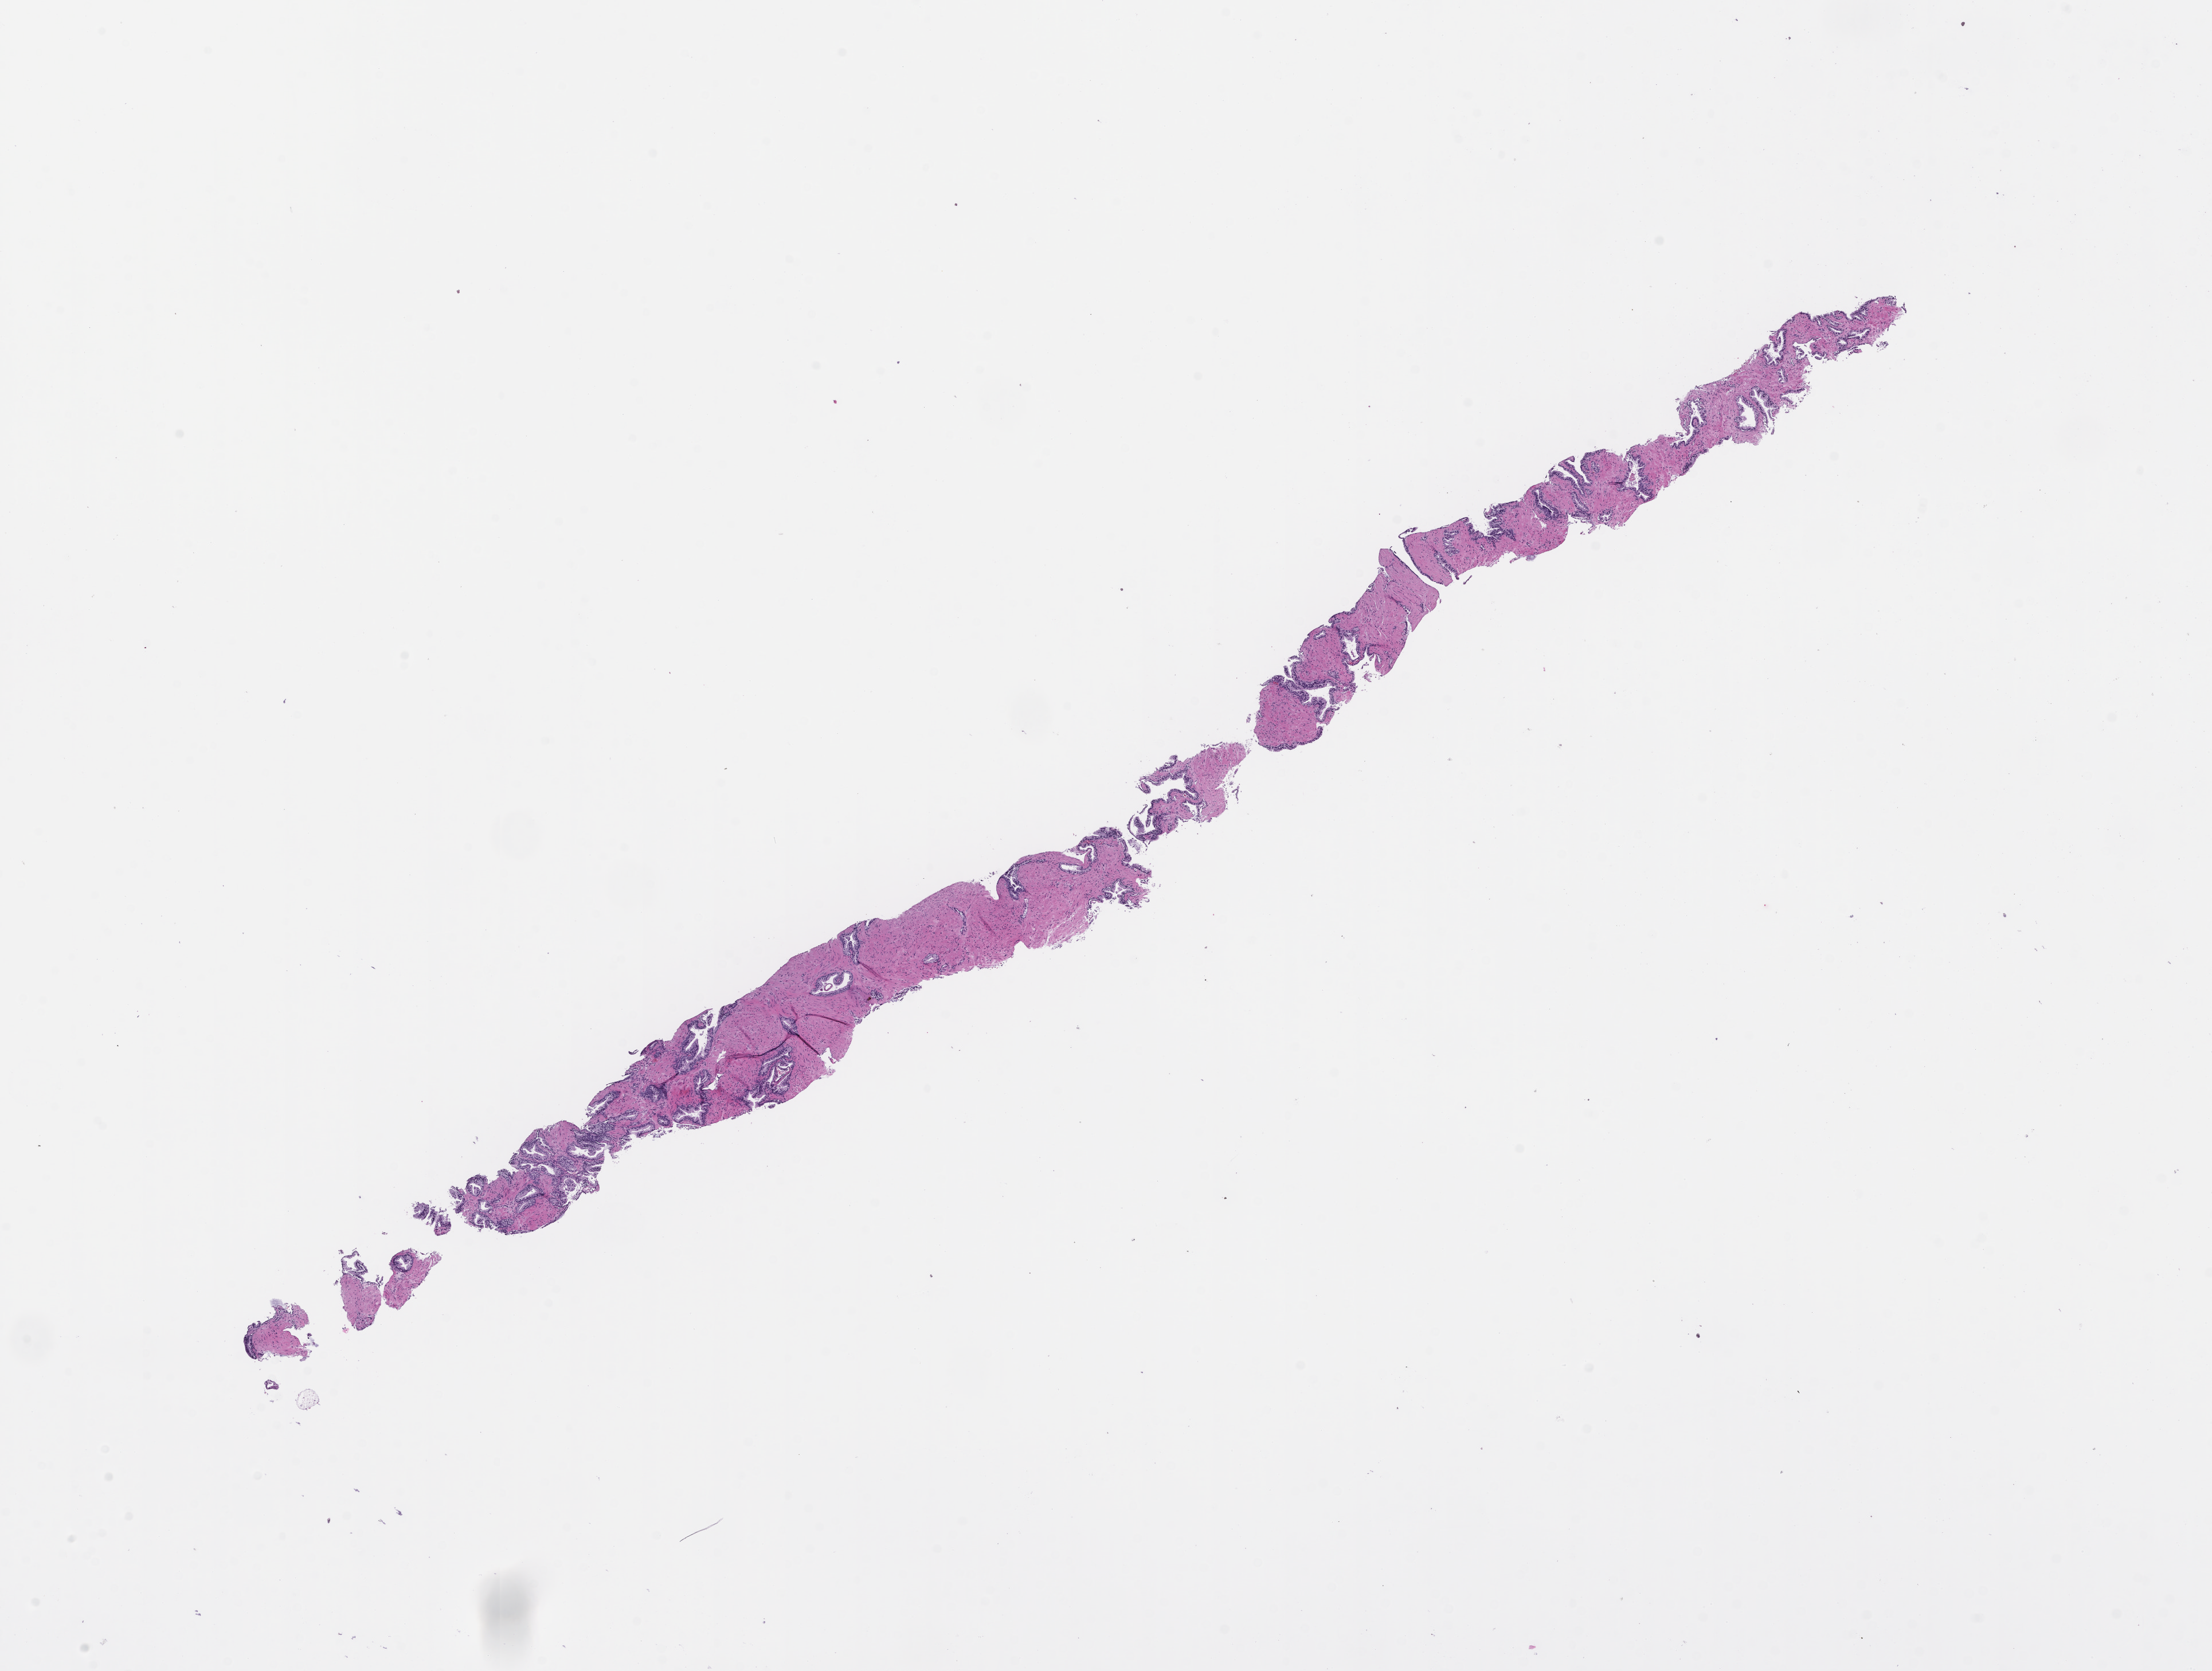
Whole-slide image, hematoxylin and eosin (H&E) stain, shown as a low-resolution overview of the whole scanned area (about 15.6 x 11.8 mm); formalin-fixed paraffin-embedded section; tissue site: prostate; collected at baseline (before treatment). Male patient.
• this section: primary tumour tissue
• diagnosis: Prostate Carcinoma